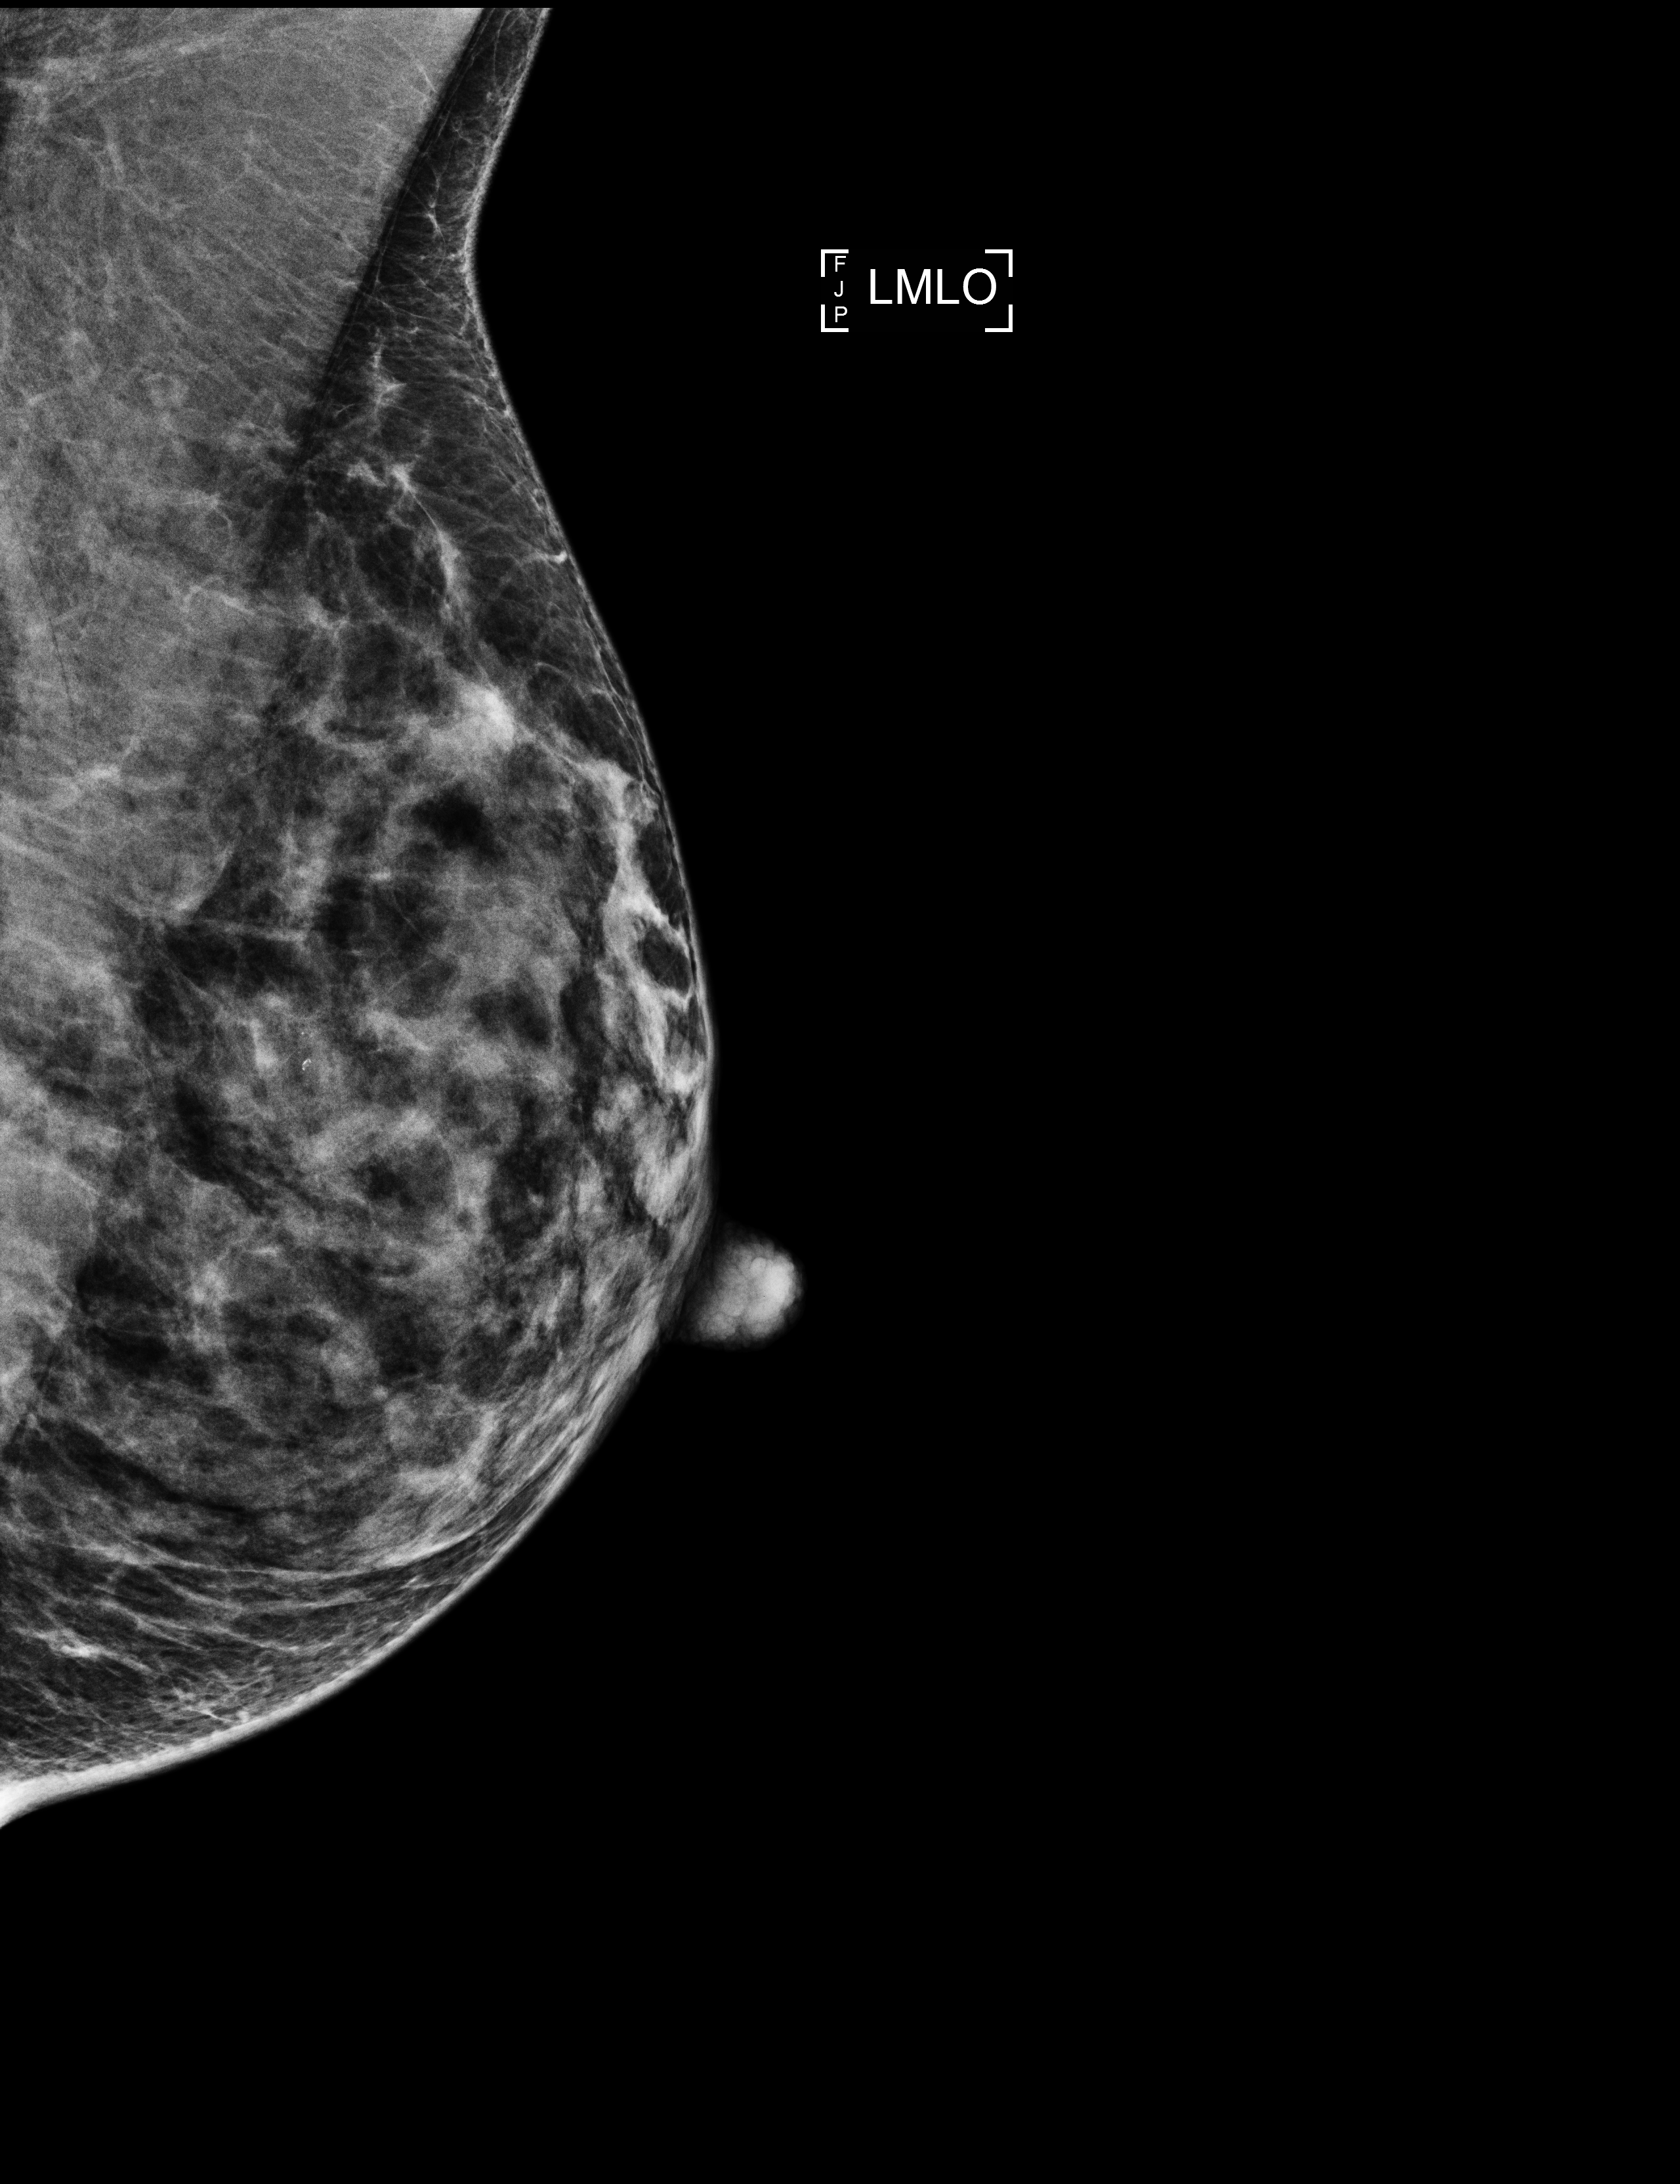
Digital mammogram (FFDM), left breast, medio-lateral oblique projection, annual screening mammography examination, compressed breast thickness 34 mm. Patient aged 53 years (female).
Breast density at the screening exam (both breasts): extremely dense (BI-RADS density category d). Final BI-RADS assessment for this screening round (tomosynthesis exam, both breasts): category 2. Recall: no recall after this screen.